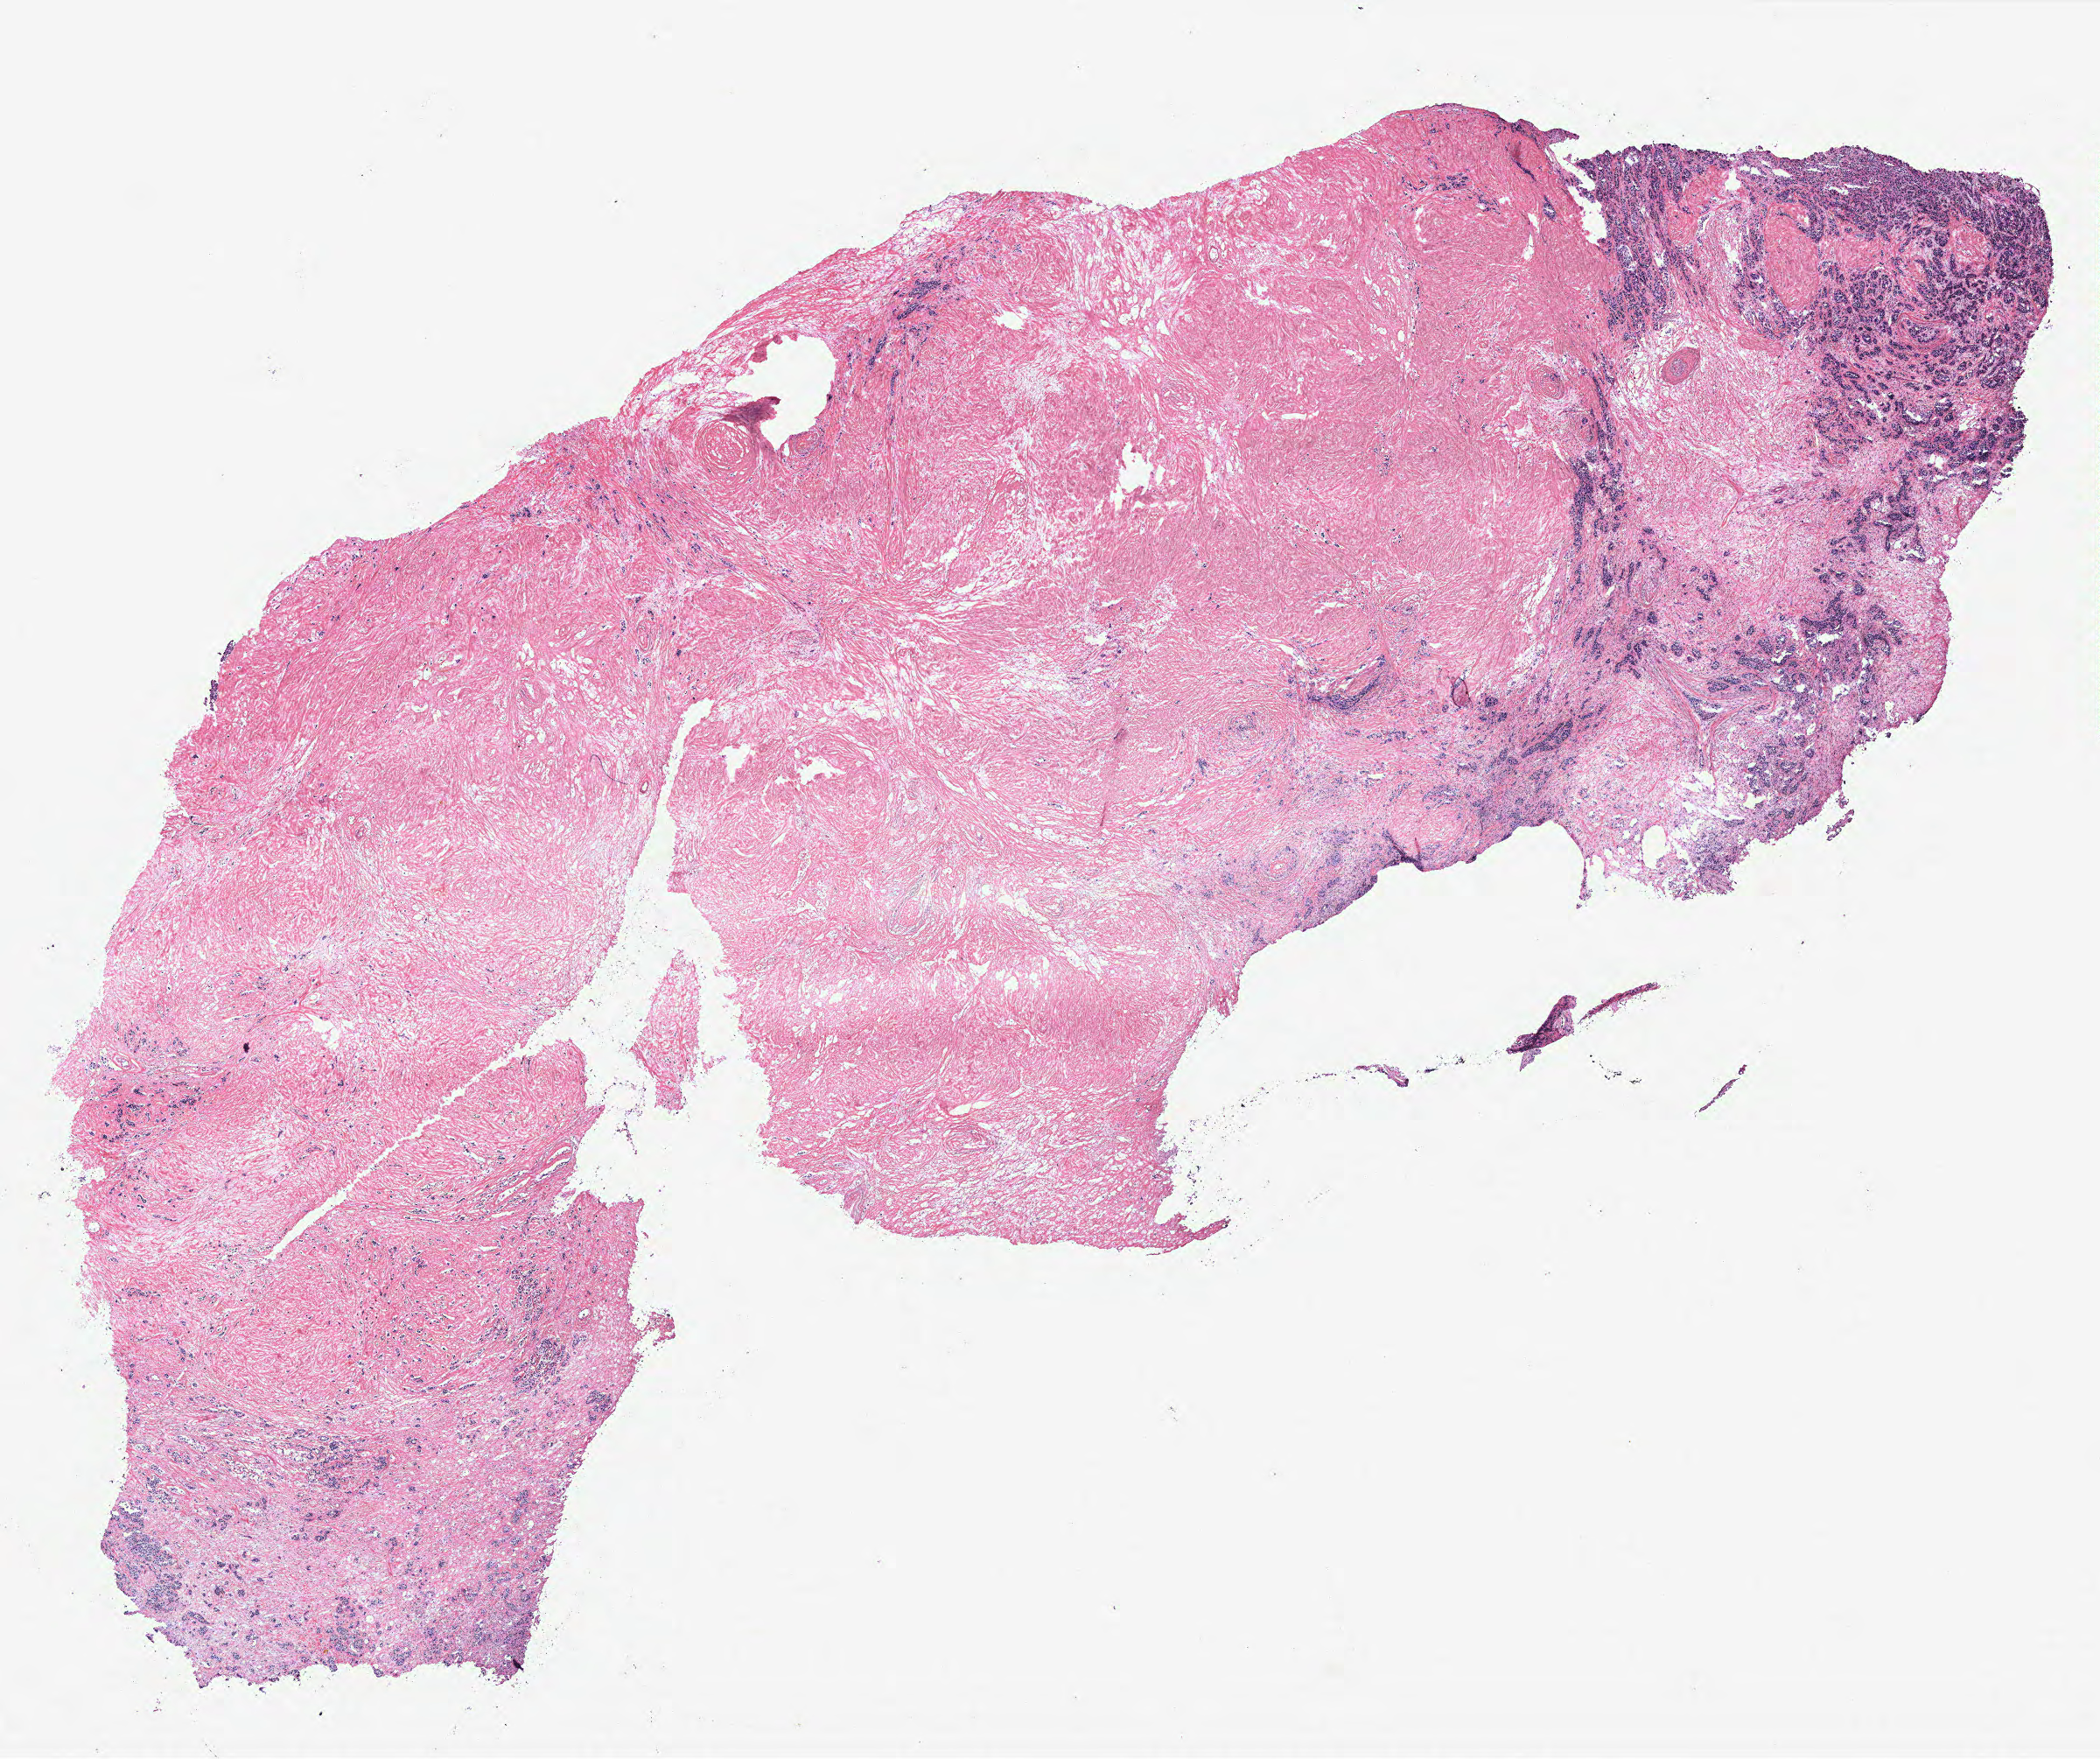
Whole-slide histology image, Hematoxylin and eosin (H&E) stained, low-resolution overview of the scanned area, about 19.2 x 16.1 mm, breast, tissue type not recorded.
- patient diagnosis (cohort enrolment): breast cancer (breast)